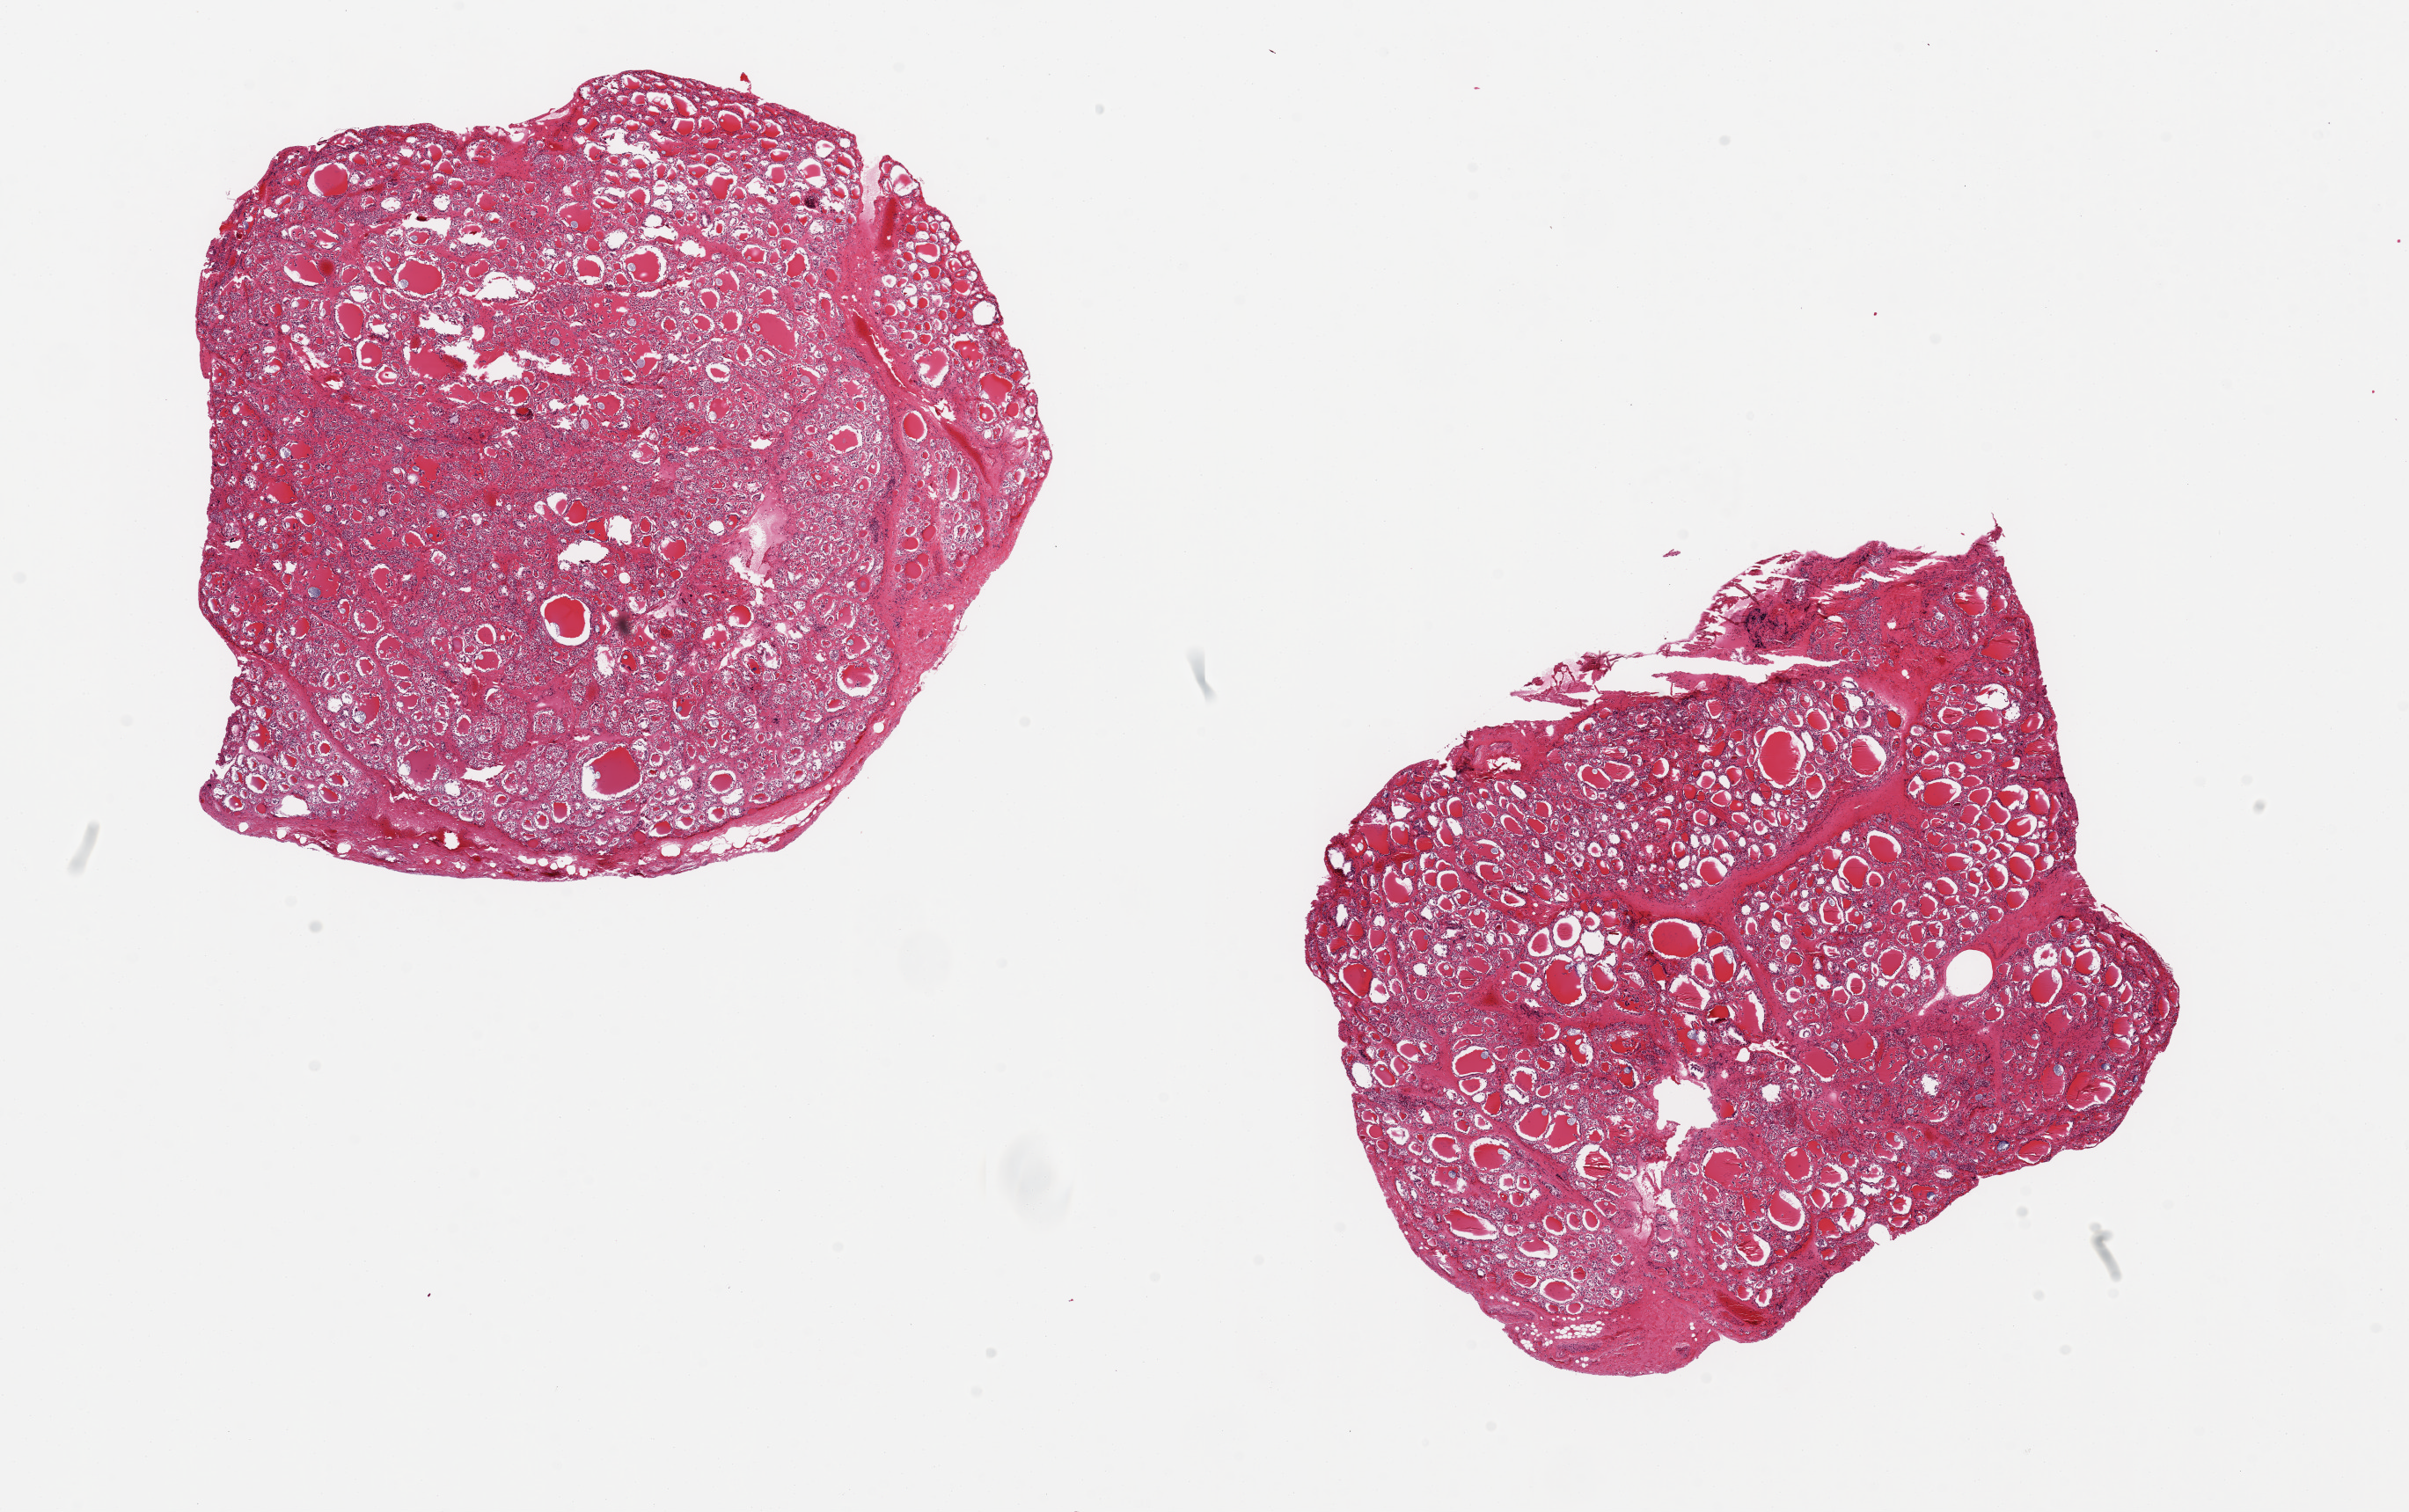
Hematoxylin and eosin (H&E) whole-slide image, low-resolution overview of the scanned area, about 21.7 x 13.6 mm (acquisition: 20x scan), PAXgene-fixed, paraffin-embedded tissue, section of thyroid (target tissue), tissue donor sample. Donor: male.
Review note (as recorded): 2 pieces 7x6 & 7x6 mm.